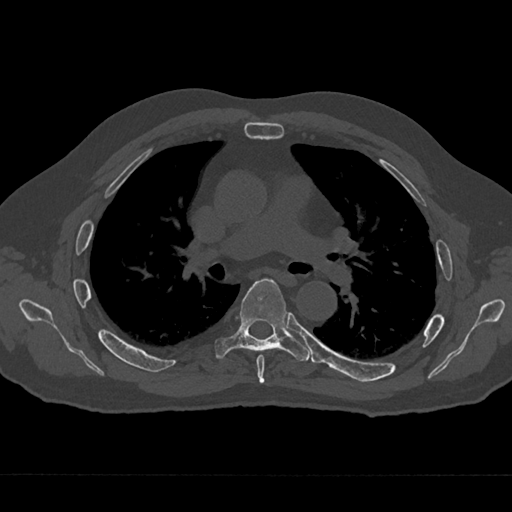
CT including the spine, one axial slice. Position 435 of 797 along the scan axis. 120 kVp. Bone window (W 1800 / L 400 HU). 0.5 mm slice thickness. 512 × 512 image matrix. Male patient, age 75 years. From the clinical record (not read from this slice): primary cancer: renal.
Annotated regions visible in this slice (semi-automatic segmentation, software-assisted and operator-edited):
- T5 vertebra: bounding box (x1, y1, x2, y2) in pixels: (256, 355, 265, 384)
- T6 vertebra: (215, 278, 310, 361)